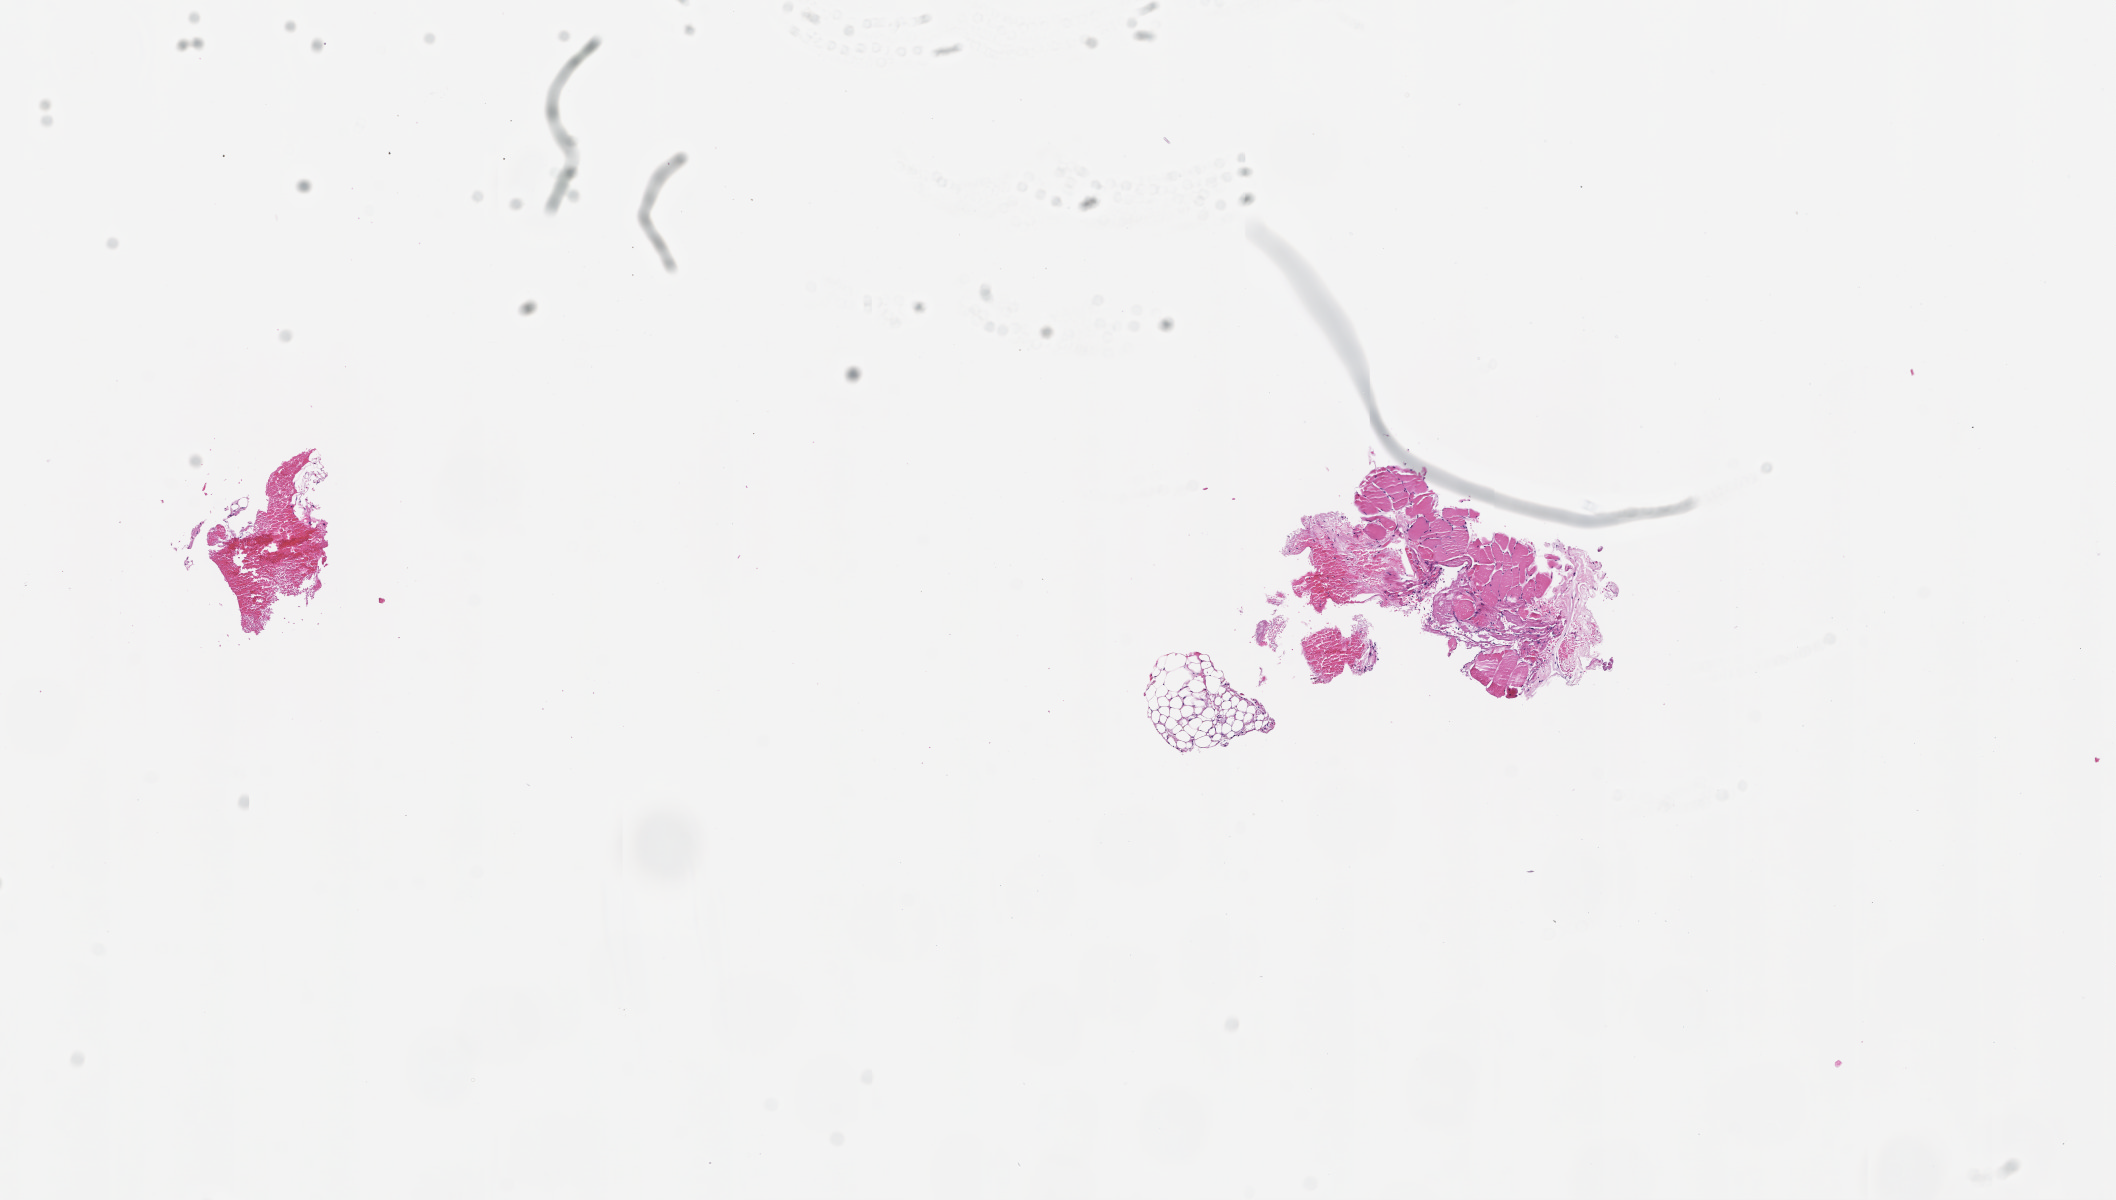
Haematoxylin and eosin whole-slide image — a low-resolution overview of the entire scanned area, about 8.5 x 4.8 mm, FFPE section, collected at baseline (before treatment). Patient sex: female.
This section: metastasis (sampled organ not recorded). Primary diagnosis of the patient: Colorectal Carcinoma.